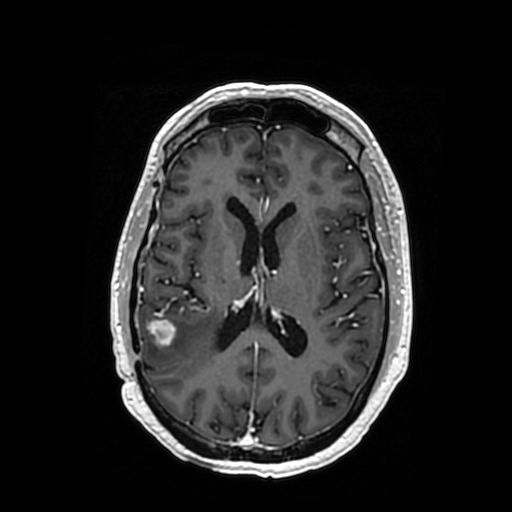
Brain MRI from a brain-tumour surgery series, one axial slice. Position 164 of 364 along the scan axis. T1-weighted post-contrast. 0.5 mm slice thickness. 512 × 512 image matrix. Case-level facts recorded for this patient, not image findings: histopathology: Oligodendroglioma; WHO grade: 3.
Structures marked on this image (outlined manually by an expert reader):
- tumour: box from (x=165, y=318) to (x=193, y=346) px